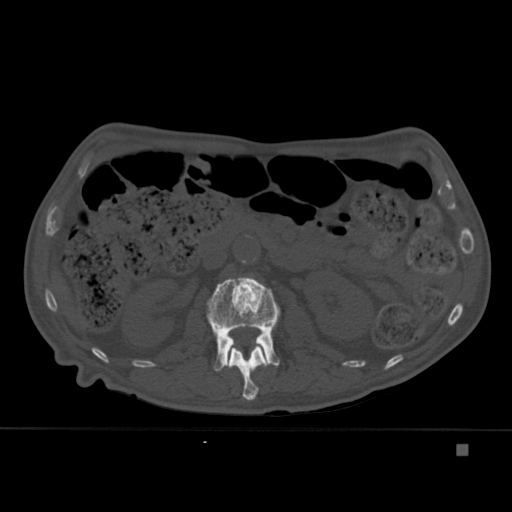
CT including the spine, one axial slice; bone window (W 1800 / L 400 HU); 1.5 mm slice thickness; 512 × 512 image matrix. Male patient, age 75 years. From the clinical record (not read from this slice): primary cancer: prostate.
Outlined on this slice (semi-automatic segmentation, software-assisted and operator-edited):
- L1 vertebra: bounding box (x1, y1, x2, y2) in pixels: (227, 345, 269, 401)
- L2 vertebra: (207, 277, 281, 372)